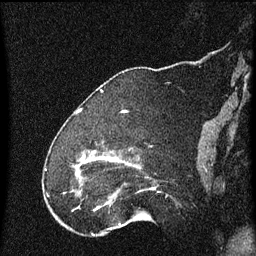
Breast MRI (dynamic contrast-enhanced), one sagittal slice. Position 17 of 60 along the scan axis. Dynamic contrast-enhanced series, image 2 of 4 at this slice position (ordered by acquisition). 1.5 T. TE 4.2 ms, TR 8 ms. 256 × 256 image matrix. Female patient, age 52 years.
Outlined on this slice (semi-automatically segmented with operator editing):
- analysis volume of interest (the breast-tissue region the enhancement analysis was run in; not a lesion): bounding box (x1, y1, x2, y2) in pixels: (73, 150, 164, 219)
- tumour enhancement mask (voxels above the 70 % enhancement threshold inside the analysis volume of interest): (76, 160, 98, 209)